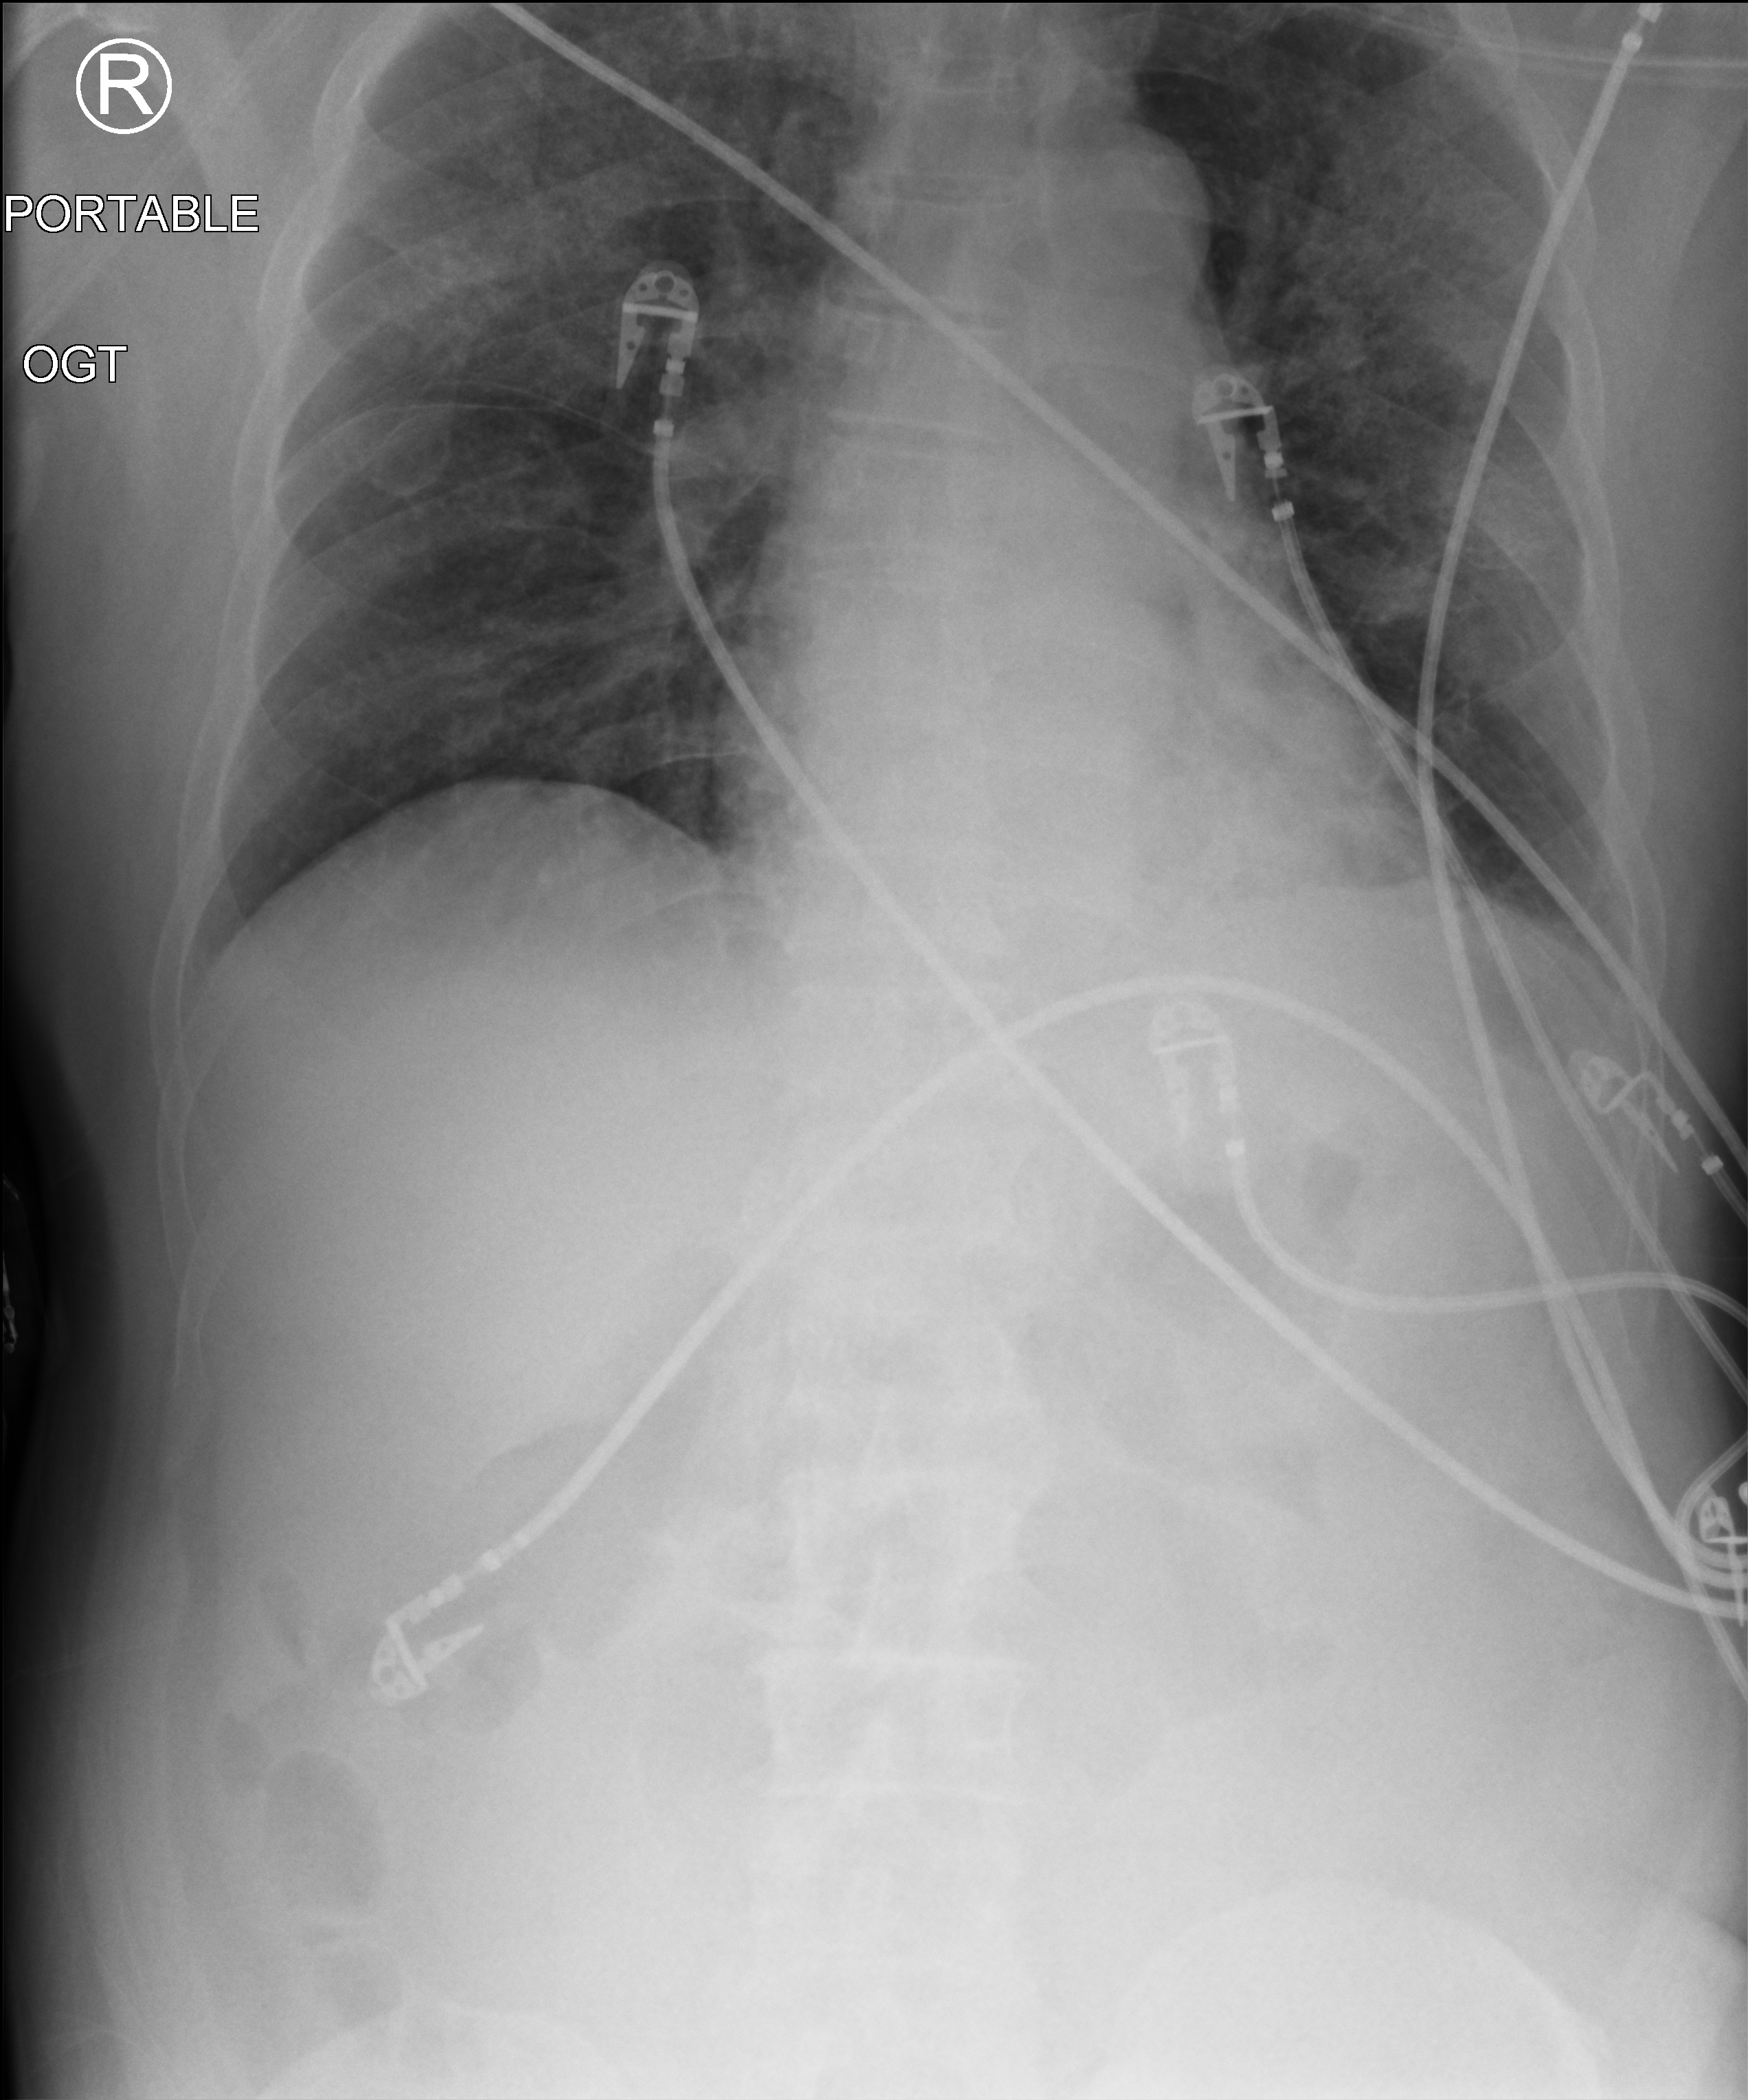
Portable chest radiograph. Male patient hospitalised with COVID-19, age 60–74 years.
From the hospital-stay record, not from the radiograph (when in the stay this image was taken is not recorded): mechanically ventilated during this hospital stay: yes; smoking status (admission record): former; admitted to intensive care during this hospital stay: yes.